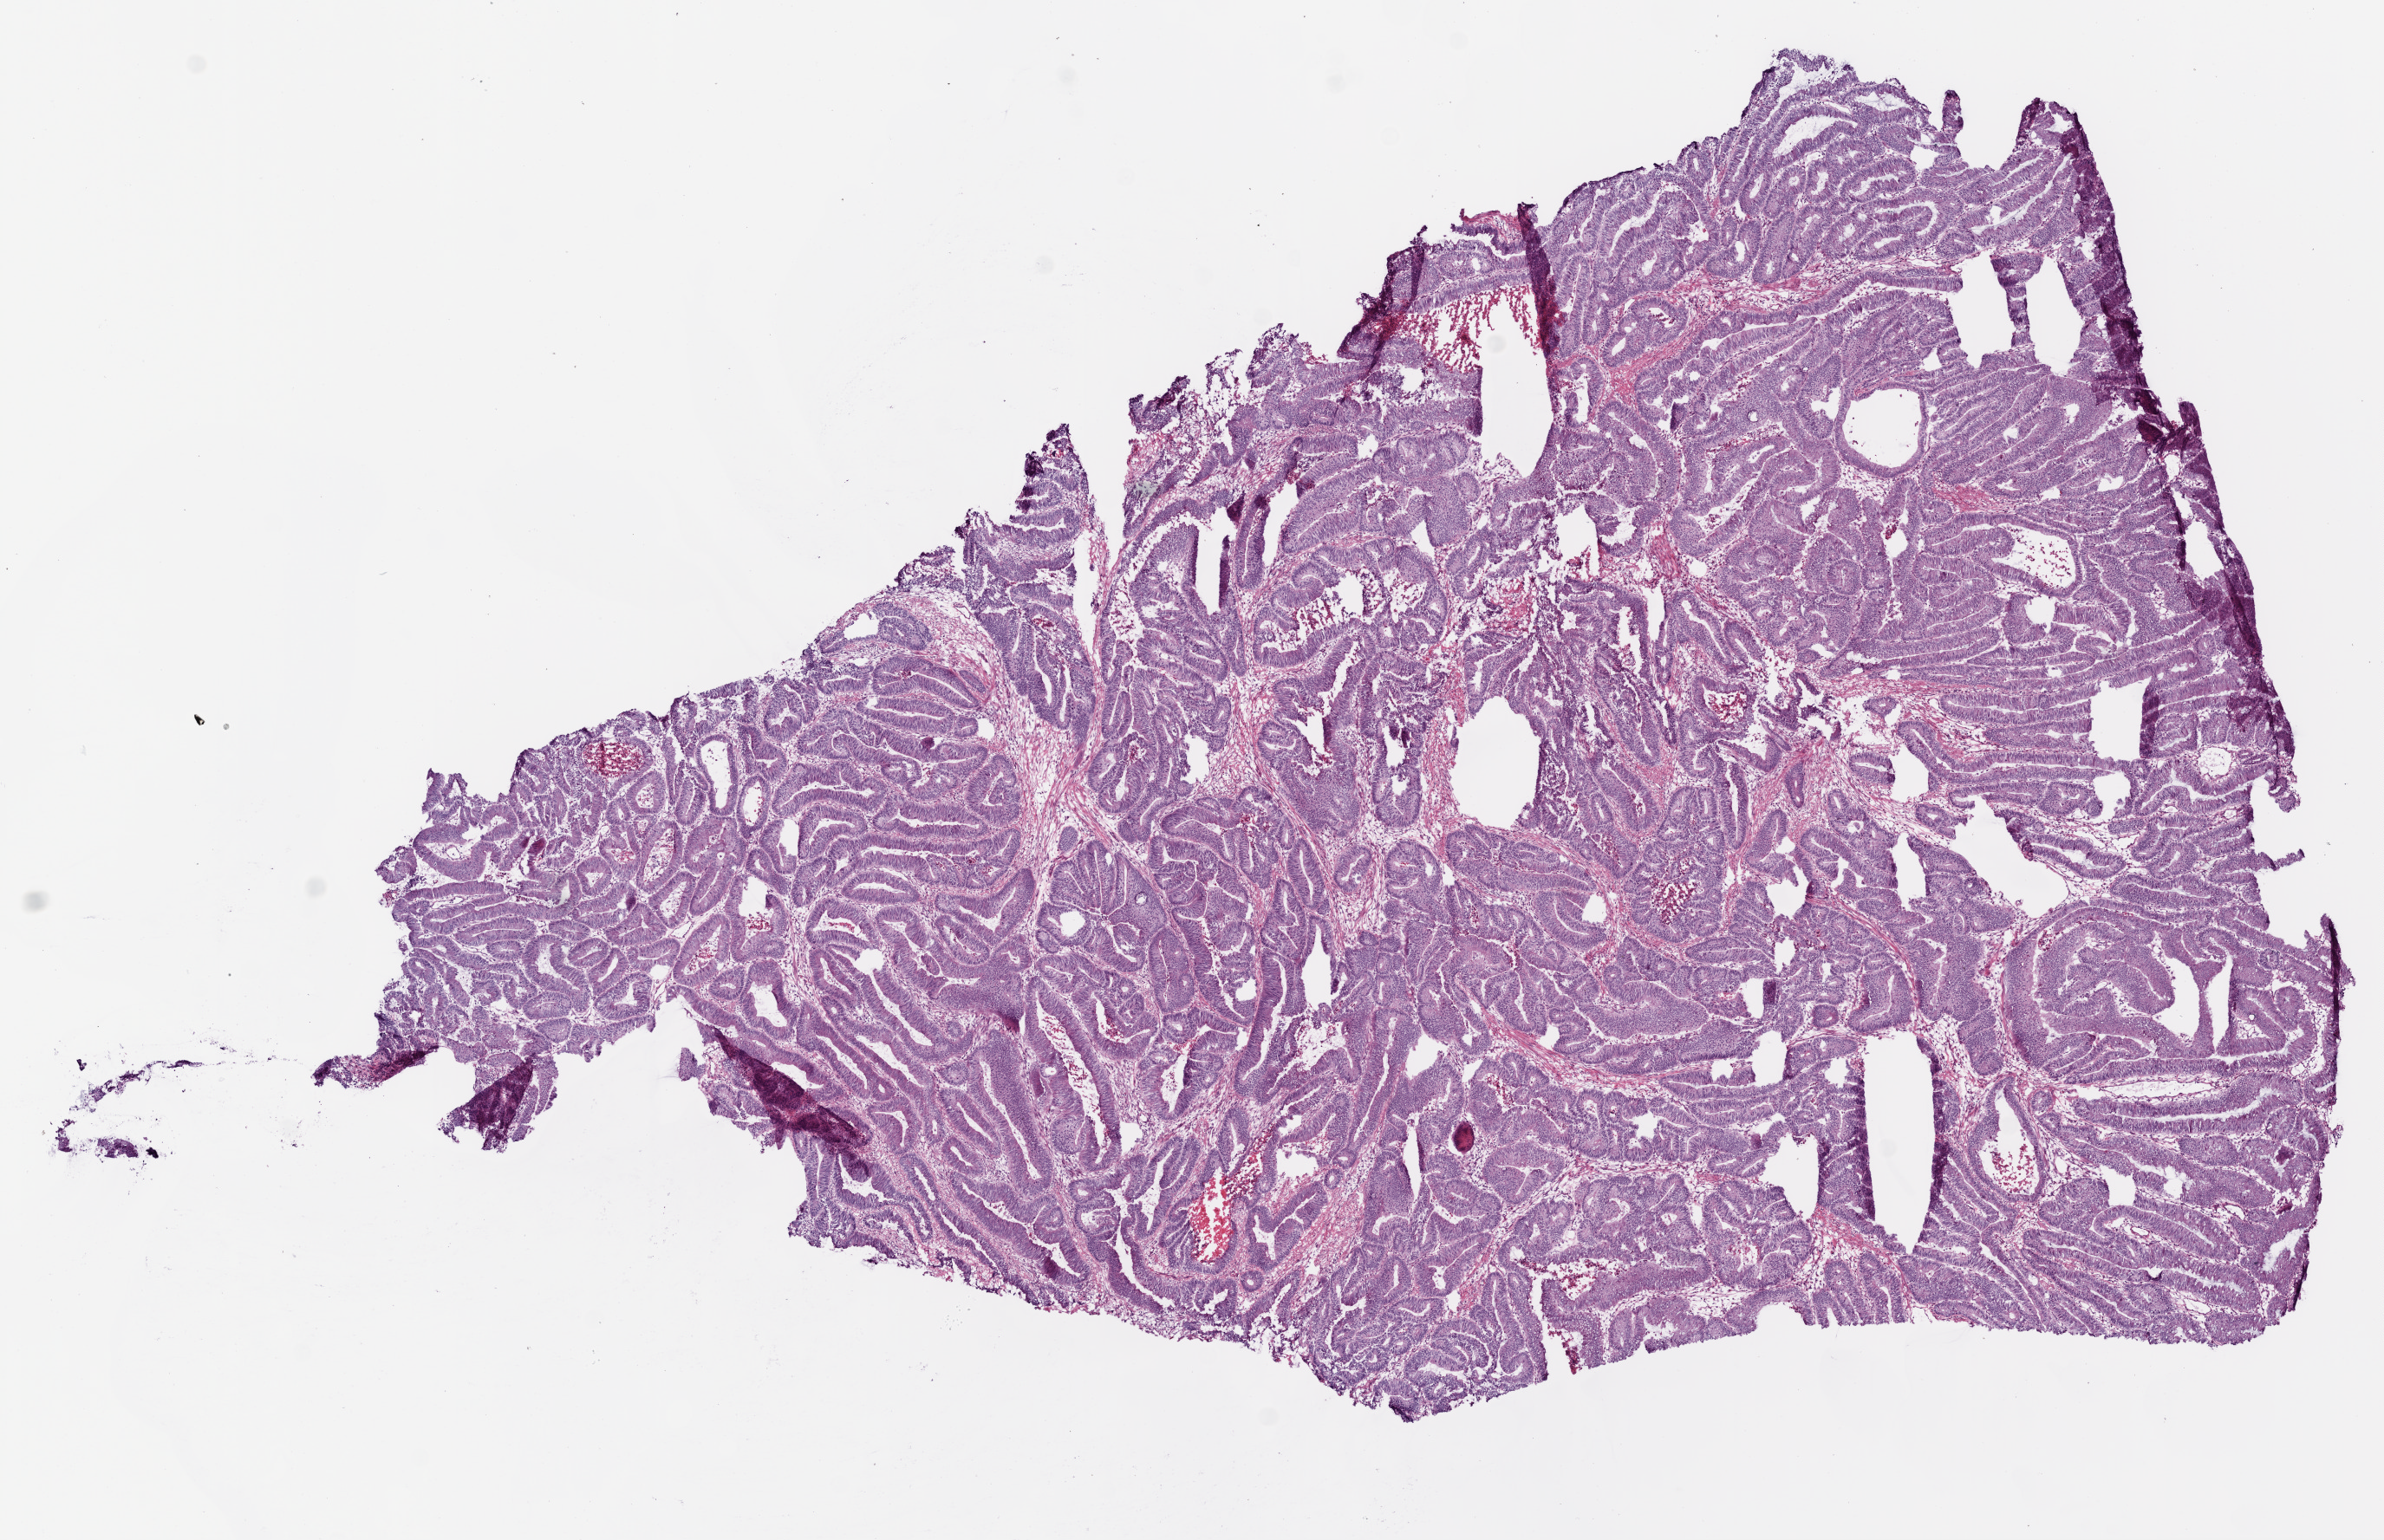
H&E whole-slide image — low-resolution overview of the scanned area, about 11.0 x 7.1 mm; frozen section; sample: primary tumour, colon. Female, age 75 years at initial diagnosis. Pathologist review of this section (percent, as recorded): tumour cells 80%, tumour nuclei 80%, normal cells 0%, stromal cells 10%, necrosis 10%.
Histologic diagnosis: Adenocarcinoma, NOS (sigmoid colon). AJCC pathologic stage: IV. Lymph nodes positive (case pathology): 1 of 26 examined.